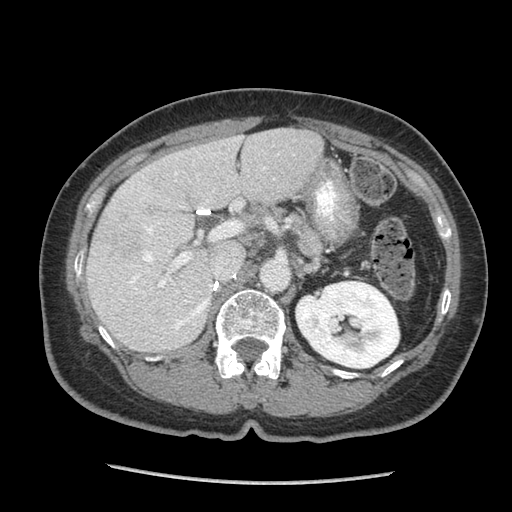
Contrast-enhanced abdominal CT (liver protocol), one axial slice; slice 45 of 105 in the series (ordered by position); soft-tissue window (W 400 / L 40 HU); 2.5 mm slice thickness; 512 × 512 image matrix. Case-level facts recorded for this patient, not image findings: diagnosis: hepatocellular carcinoma (patient treated with transarterial chemoembolisation; whether this scan precedes or follows treatment is not stated here); TNM stage (as recorded): Stage-I; Child-Pugh class: A; tumour differentiation: moderately differentiated; tumour nodularity: uninodular.
Structures marked on this image (semi-automatically segmented with operator editing):
- liver parenchyma outside the tumour (the mass and vessels are separate outlines, so this box may not span the whole liver): bounding box (x1, y1, x2, y2) in pixels: (86, 128, 324, 350)
- liver vessels: (122, 167, 266, 330)